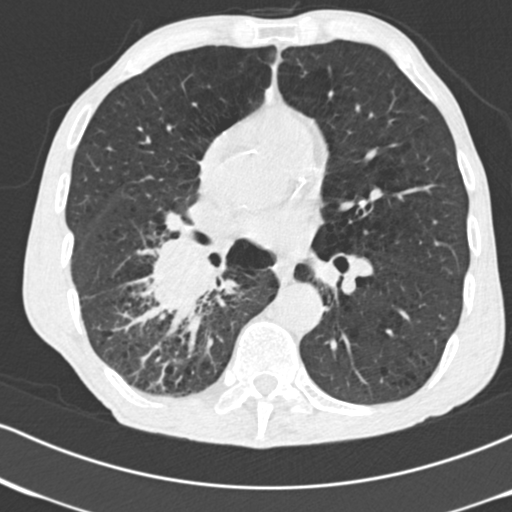
Low-dose screening chest CT, one axial slice; reconstruction kernel B30f; 120 kVp; lung window (W 1500 / L -600 HU); 2 mm slice thickness; 512 × 512 image matrix, field of view 316 × 316 mm.
Structures marked on this image (expert manual segmentation):
- lesion 1 (tumor, lower lobe of right lung): bounding box (x1, y1, x2, y2) in pixels: (148, 242, 220, 315)